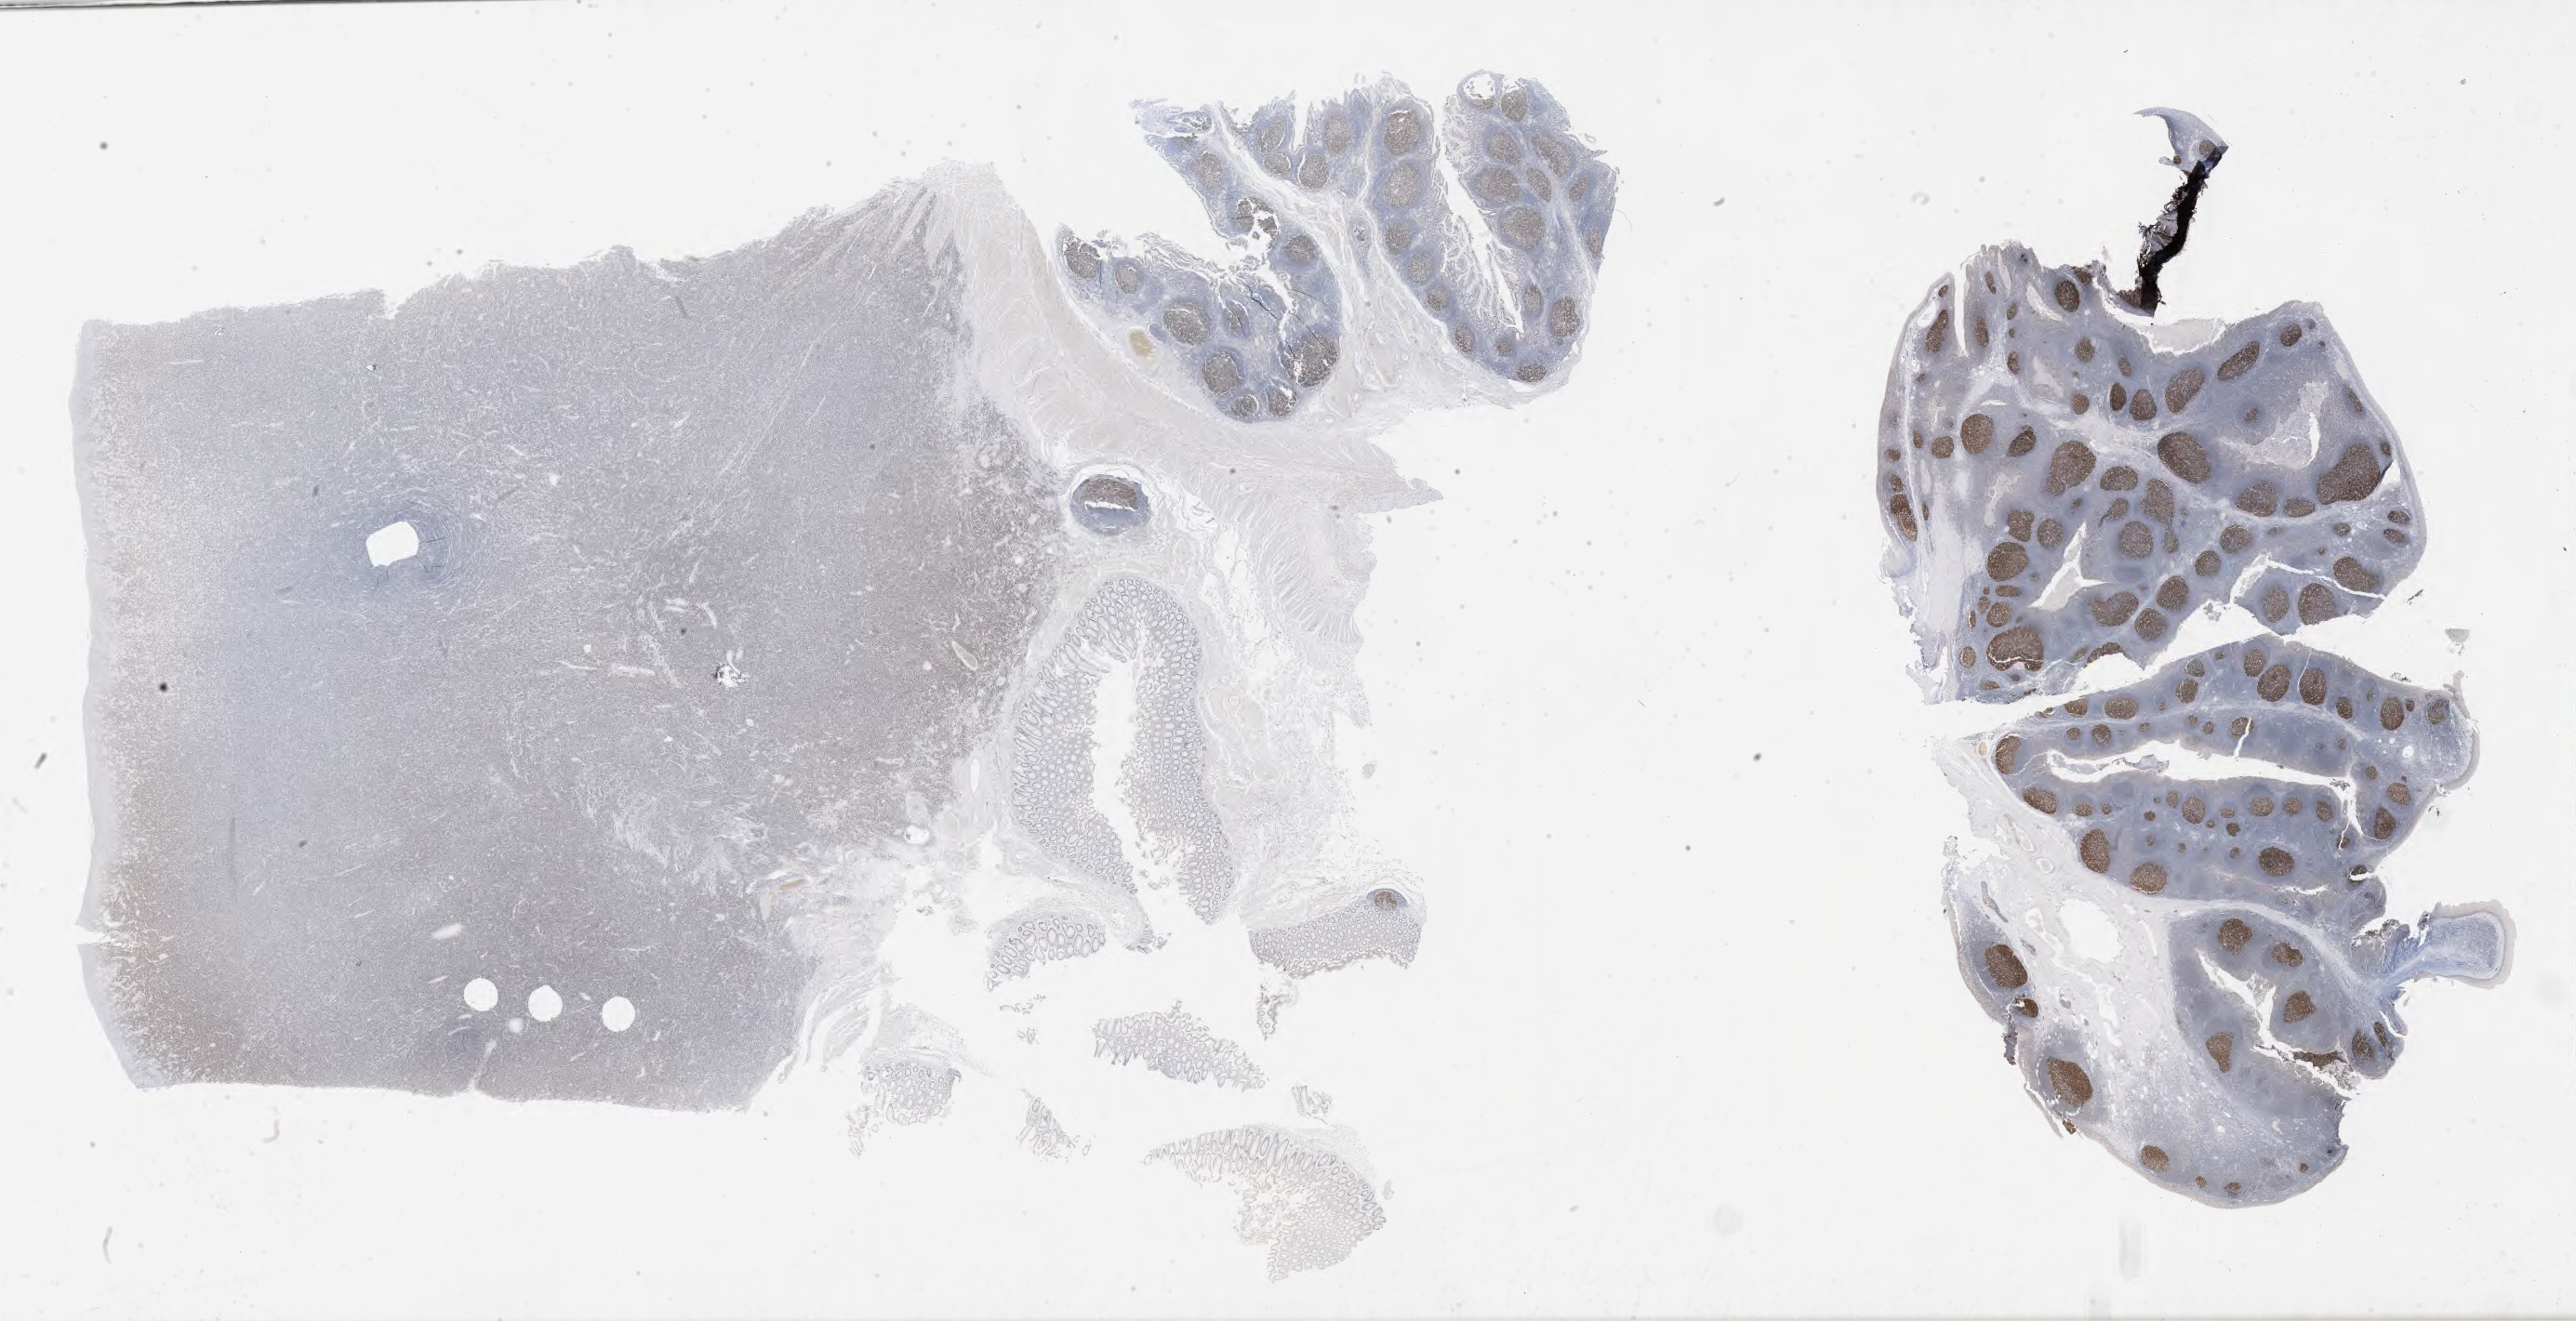
Whole-slide image, immunohistochemical stain for BCL6 — a low-resolution overview of the entire scanned area, about 44.8 x 23.0 mm, tumor tissue. Male patient; age at initial diagnosis 7 years.
Diagnosis: Burkitt lymphoma, NOS.